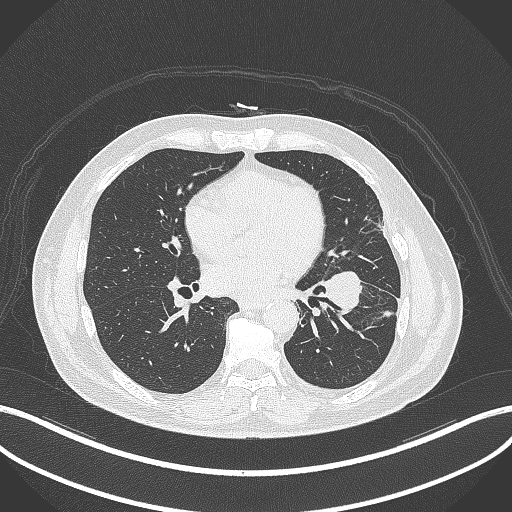
Chest CT, one axial slice; position 162 of 230 along the scan axis; reconstruction kernel B70f; lung window (W 1500 / L -600 HU); 1 mm slice thickness; 512 × 512 image matrix, field of view 400 × 400 mm. Patient: male, 68 years. Case-level facts recorded for this patient, not image findings: clinical TNM (as recorded): T2b N0 M0.
Annotated regions visible in this slice (rectangle marked by the reading radiologist):
- lung tumour (recorded histology: squamous cell carcinoma): bounding box (x1, y1, x2, y2) in pixels: (321, 268, 366, 315)